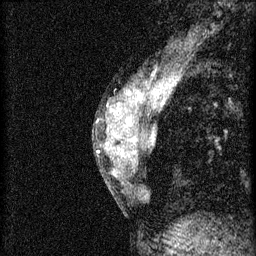
Breast MRI (dynamic contrast-enhanced), one sagittal slice. Slice 23 of 46 in the series (ordered by position). 3 images stored at this slice position (order not interpretable as contrast timing). 1.5 T. TE 4.2 ms, TR 8.2 ms. 256 × 256 image matrix, field of view 180 × 180 mm. Patient: female, 44 years.
Outlined on this slice (semi-automatic segmentation, software-assisted and operator-edited):
- analysis volume of interest (the breast-tissue region the enhancement analysis was run in; not a lesion): bounding box [x1, y1, x2, y2] px = [110, 128, 154, 181]
- tumour enhancement mask (voxels above the 70 % enhancement threshold inside the analysis volume of interest): [122, 138, 154, 157]